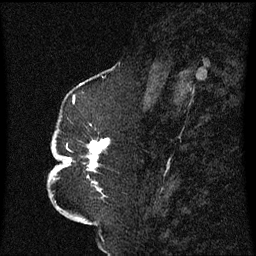
Breast MRI (dynamic contrast-enhanced), one sagittal slice. Position 26 of 60 along the scan axis. Dynamic contrast-enhanced series, image 2 of 3 at this slice position (ordered by acquisition). 1.5 T. TE 4.2 ms, TR 8.4 ms. 2.3 mm slice thickness. 256 × 256 image matrix, field of view 200 × 200 mm. Female patient, age 52 years. Case-level facts recorded for this patient, not image findings: setting: breast cancer imaged before/during neoadjuvant chemotherapy; receptor status: HR-positive, HER2-negative.
Annotated regions visible in this slice (semi-automatically segmented with operator editing):
- analysis volume of interest (the breast-tissue region the enhancement analysis was run in; not a lesion): bounding box (x1, y1, x2, y2) in pixels: (49, 124, 111, 197)
- tumour enhancement mask (voxels above the 70 % enhancement threshold inside the analysis volume of interest): (63, 138, 110, 187)